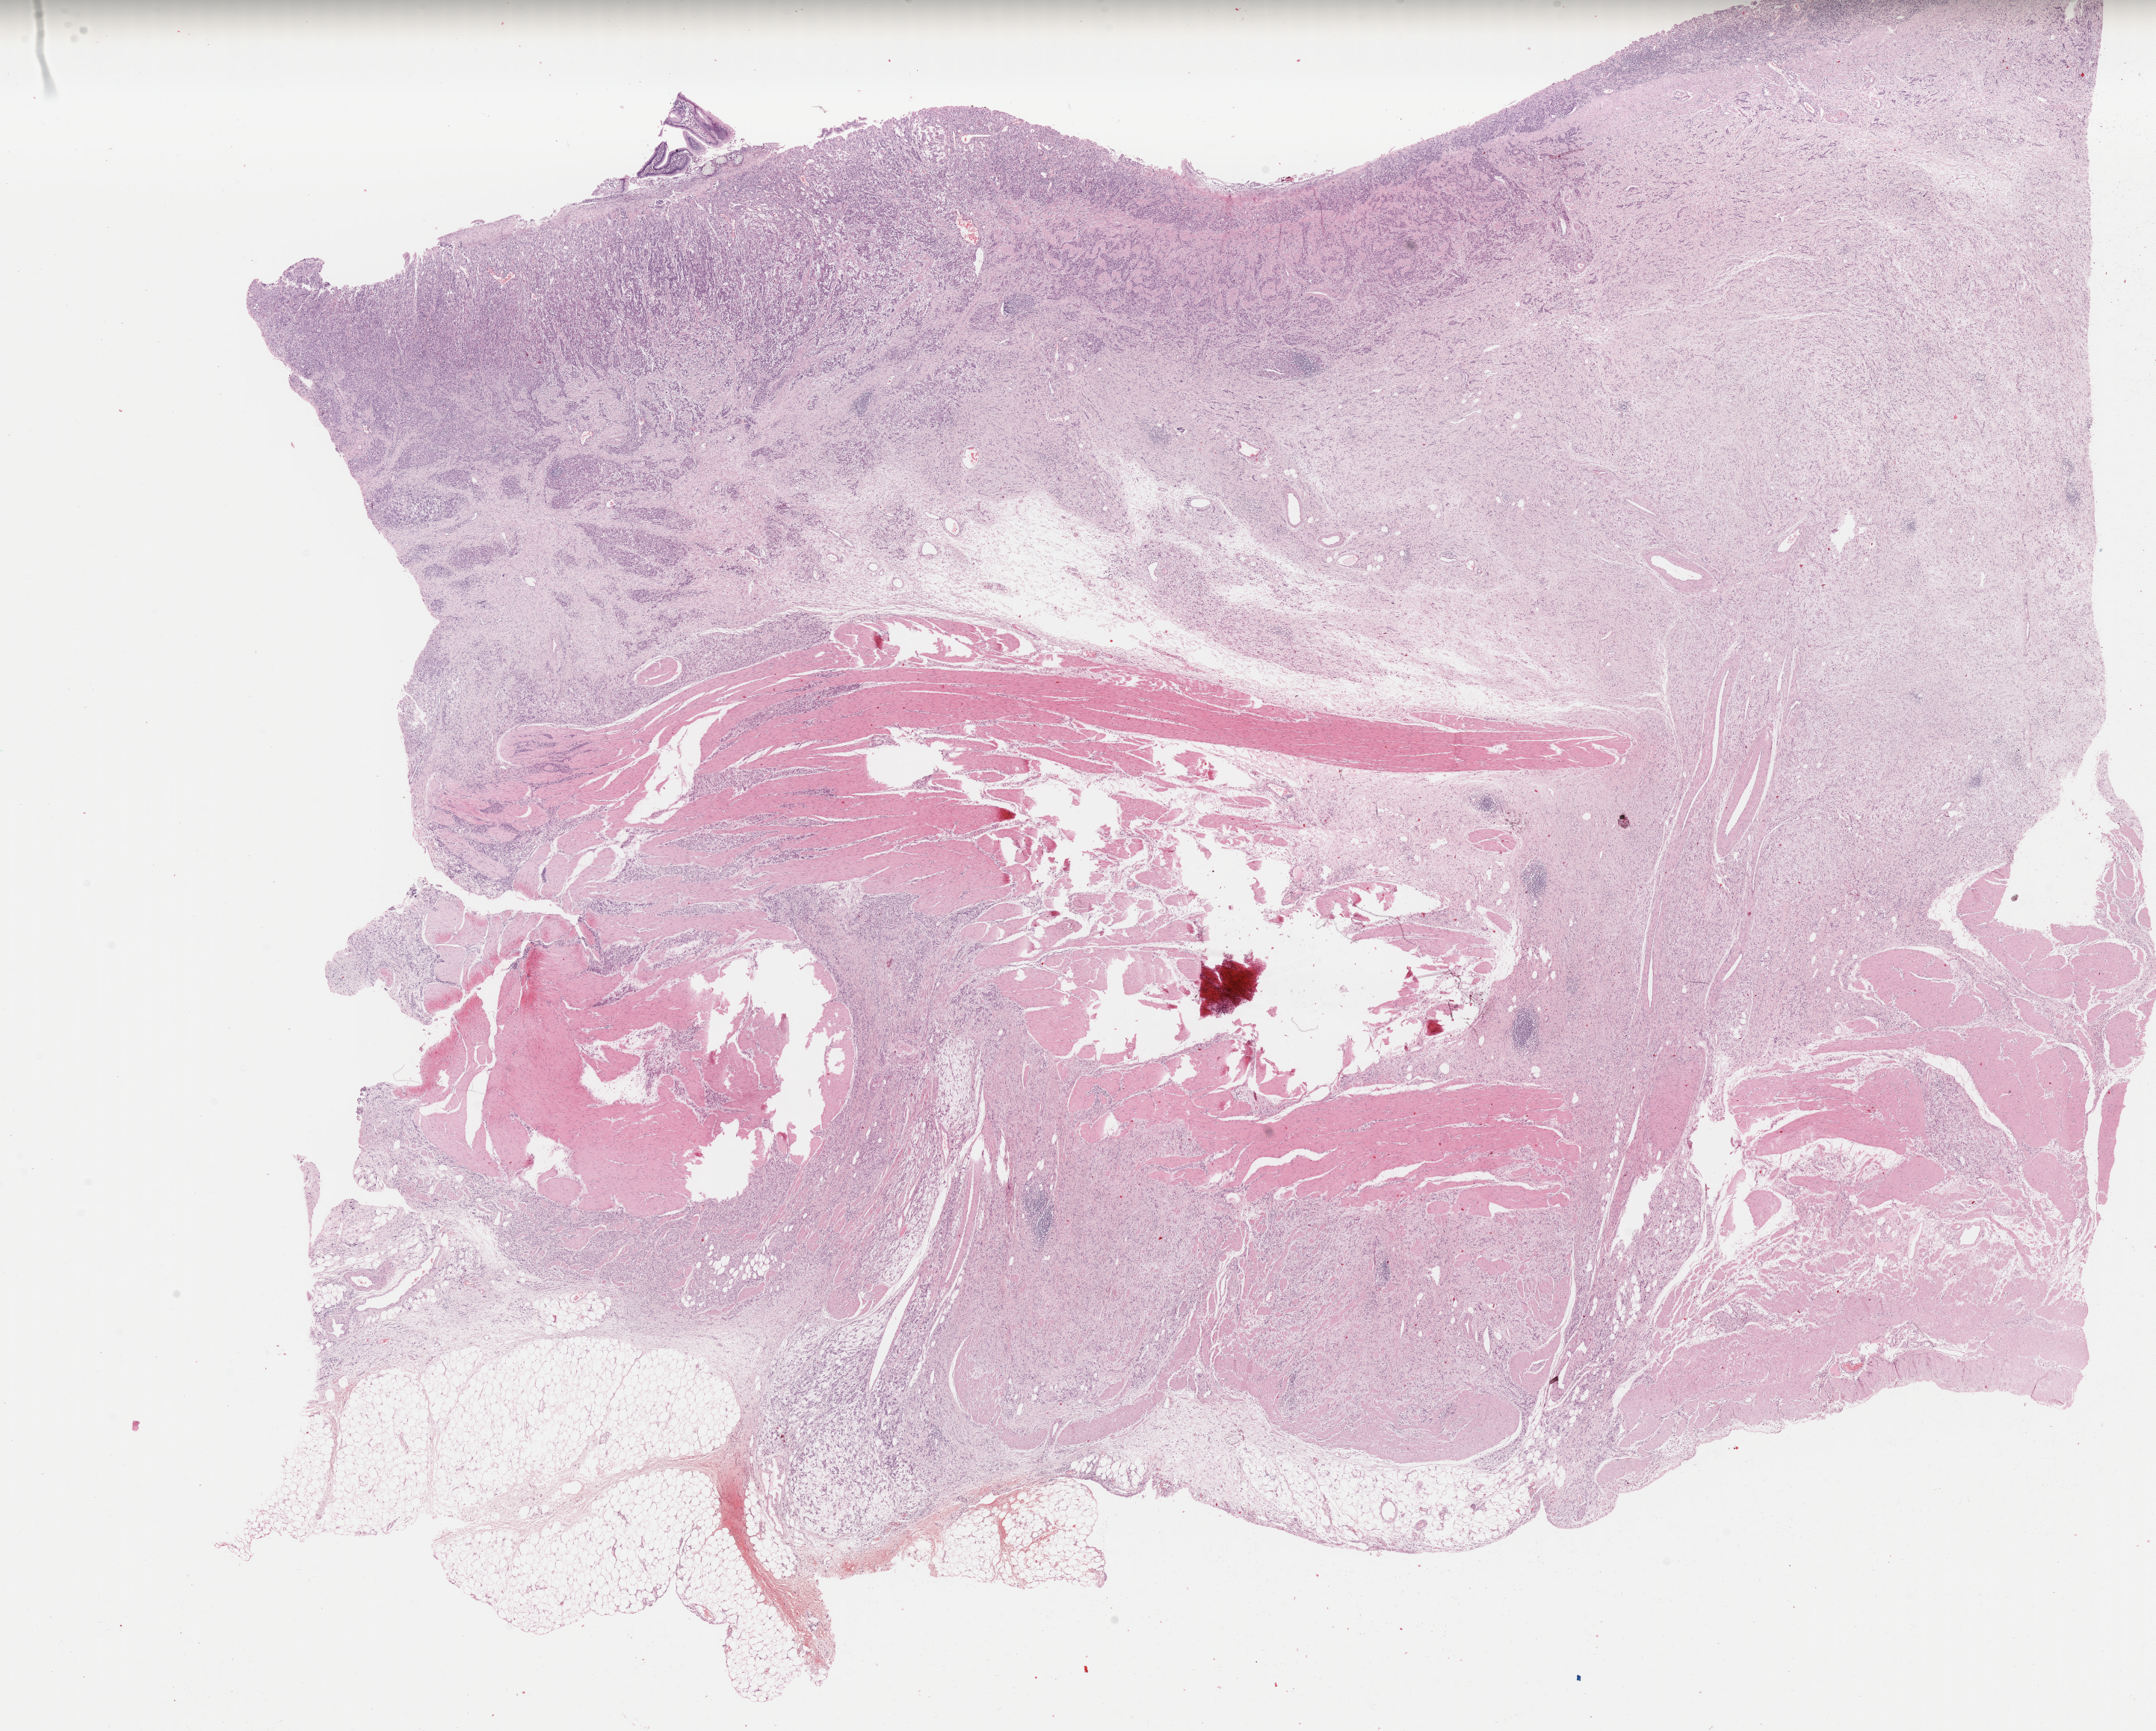
Digitized H&E tissue section (whole slide), low-resolution overview of the scanned area, about 22.8 x 18.3 mm. FFPE section. Sample: primary tumour, stomach. Male, age 72 years at initial diagnosis. Histologic grade: G2 (moderately differentiated).
* histologic diagnosis: Adenocarcinoma, NOS
* AJCC pathologic stage: IB (7th edition)